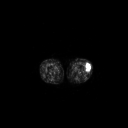
FDG PET of an extremity soft-tissue mass (from a PET/CT study), one axial slice; position 176 of 223 along the scan axis; 128 × 128 image matrix. Patient: female, 16 years. From the clinical record (not read from this slice): histological type: spindle cell suggestive of biphasic synovial sarcoma; grade: intermediate; site of the primary tumour: left knee.
Annotated regions visible in this slice (expert contour drawn on MRI and transferred to this co-registered scan by the dataset authors):
- gross tumour volume including surrounding oedema: bounding box [x1, y1, x2, y2] px = [85, 61, 91, 71]
- gross tumour volume (mass): [85, 62, 91, 71]